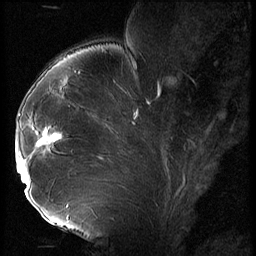
Breast MRI (dynamic contrast-enhanced), one sagittal slice. Position 37 of 56 along the scan axis. 3 images stored at this slice position (order not interpretable as contrast timing). 1.5 T. TE 4.2 ms, TR 9 ms. 2.5 mm slice thickness. 256 × 256 image matrix. Female patient, age 43 years. Case-level facts recorded for this patient, not image findings: setting: breast cancer imaged before/during neoadjuvant chemotherapy; receptor status: HER2-positive.
Outlined on this slice (semi-automatic segmentation, software-assisted and operator-edited):
- analysis volume of interest (the breast-tissue region the enhancement analysis was run in; not a lesion): box from (x=17, y=92) to (x=74, y=211) px
- tumour enhancement mask (voxels above the 140 % enhancement threshold inside the analysis volume of interest): (x=17, y=126)–(x=63, y=193)